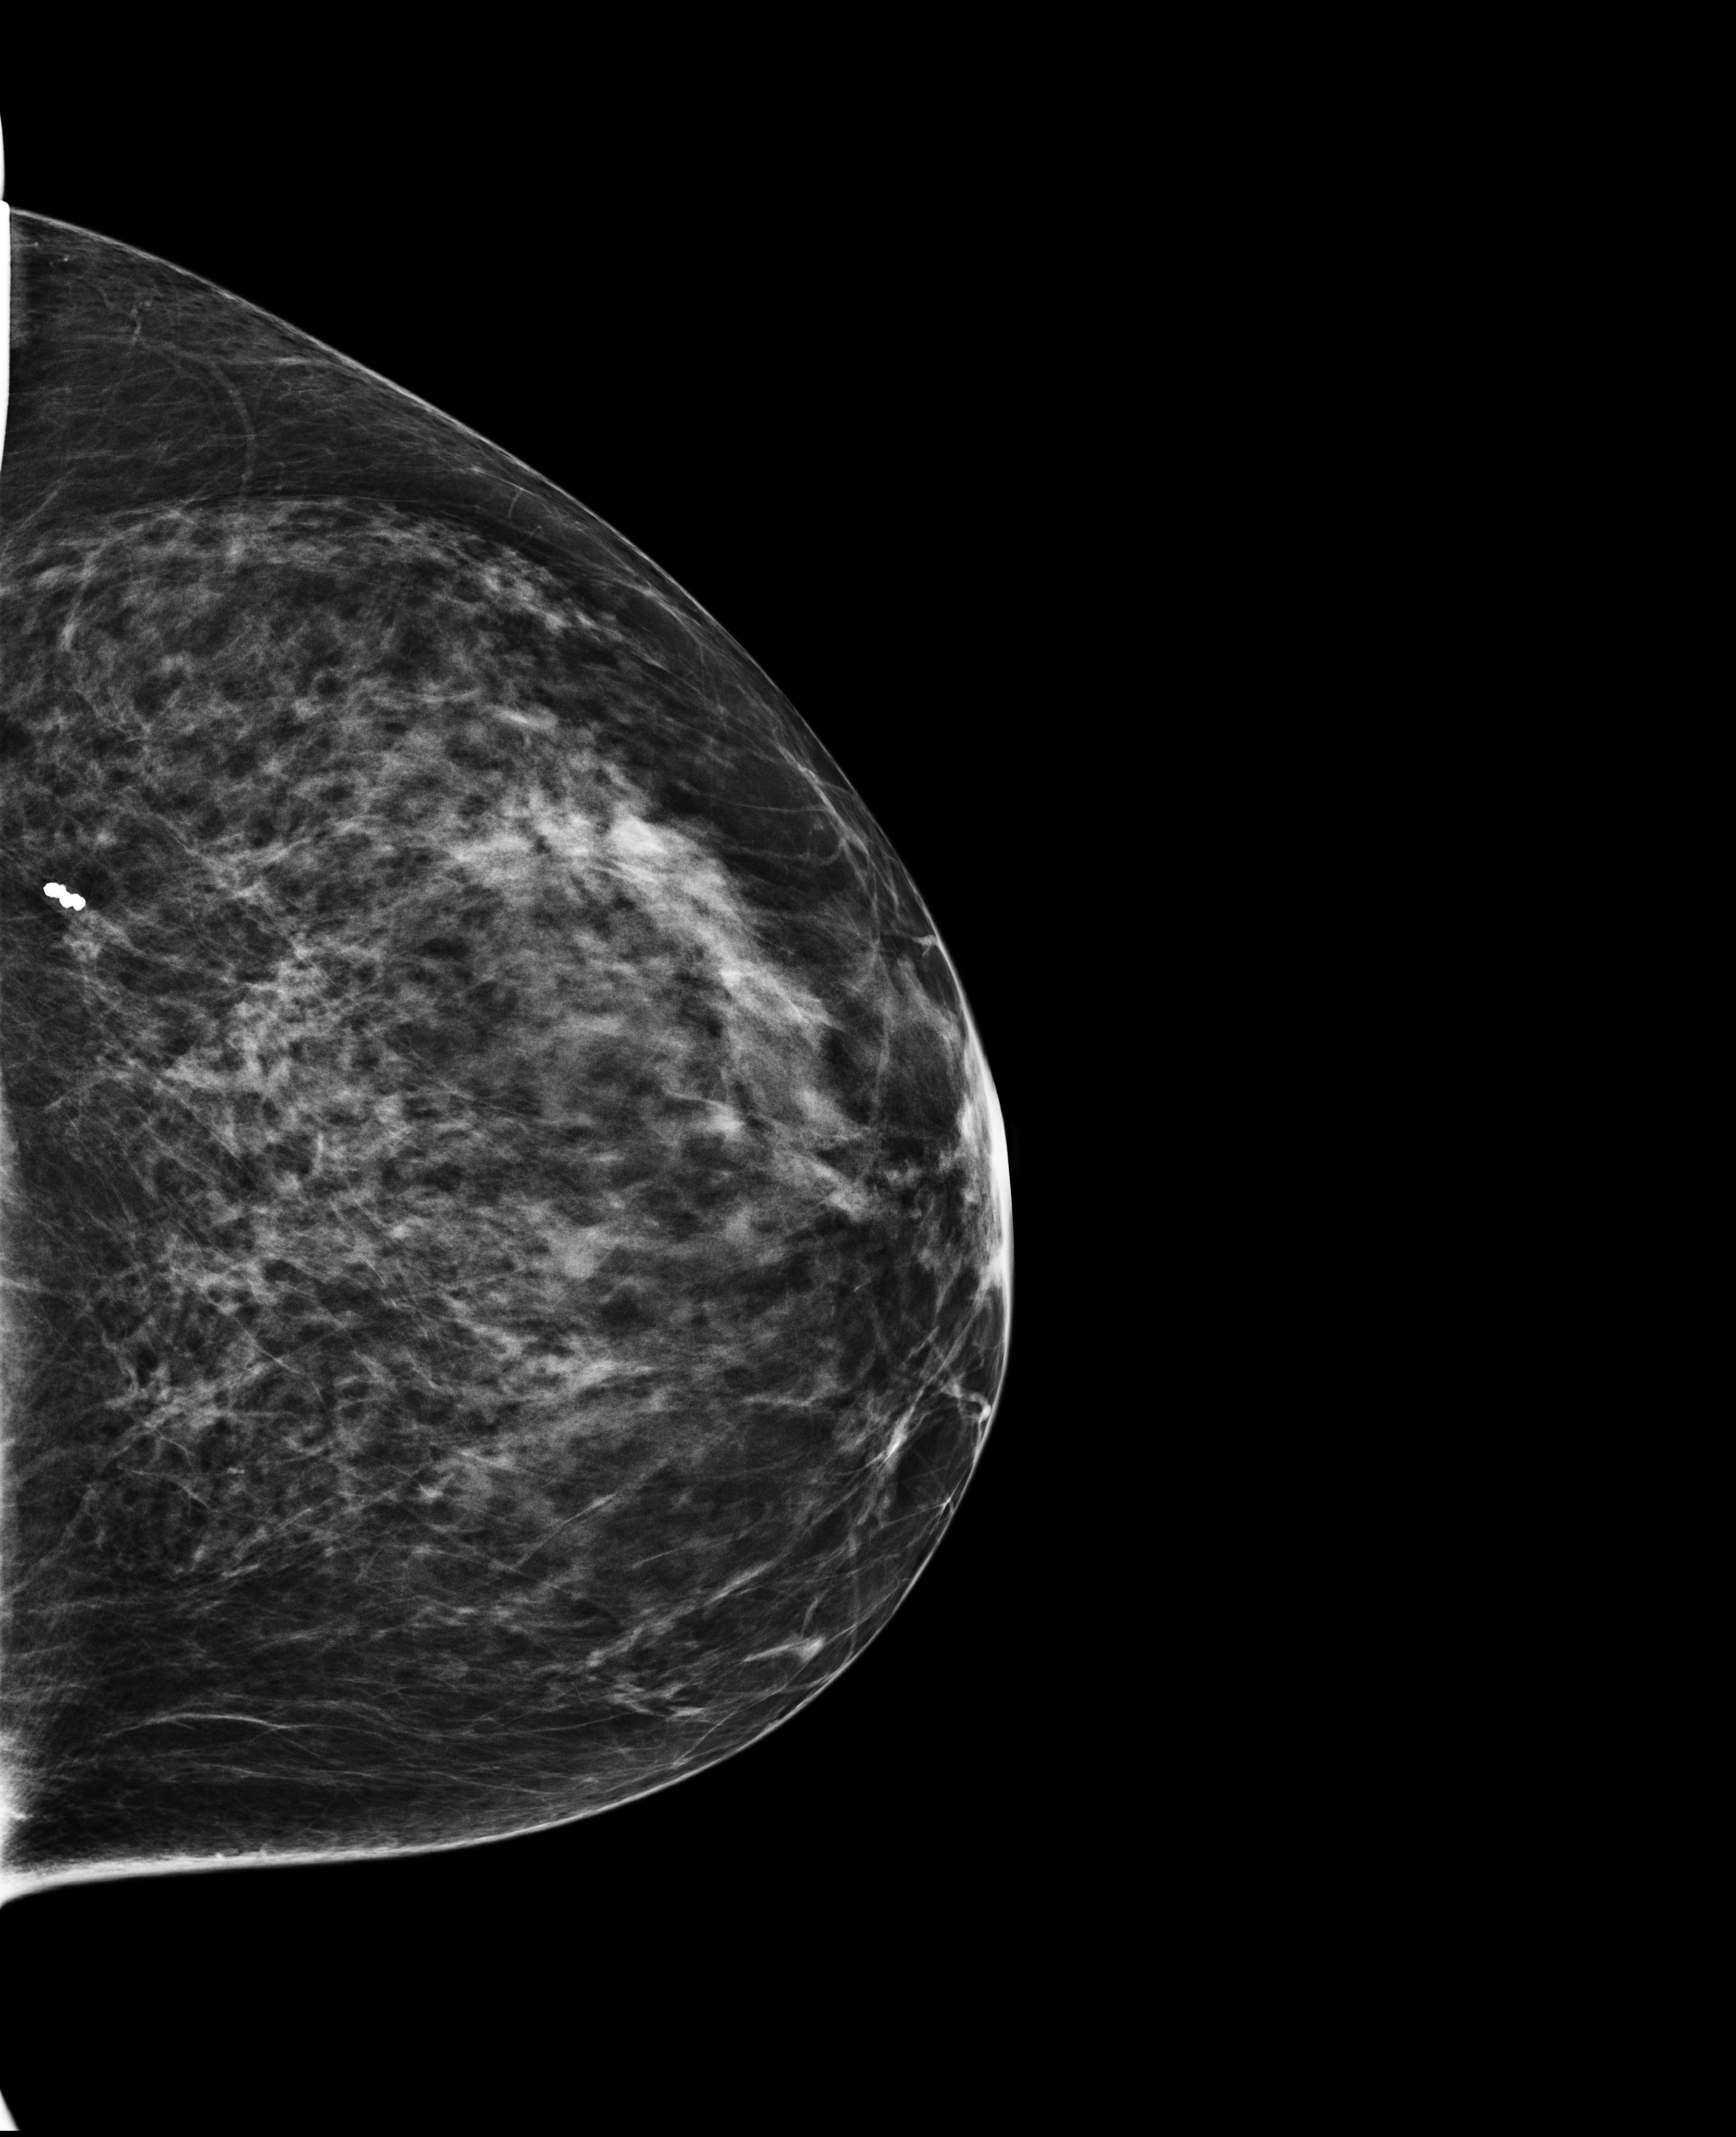
Full-field digital mammogram (FFDM); left breast; craniocaudal (CC) view; screening examination; compressed breast thickness 64 mm. Female patient, age 61 years.
BI-RADS breast density category at the screening exam (both breasts, scale 1–4): 2. Final BI-RADS assessment for this screening round (tomosynthesis exam, both breasts): category 1. Recall: no recall after this screen.